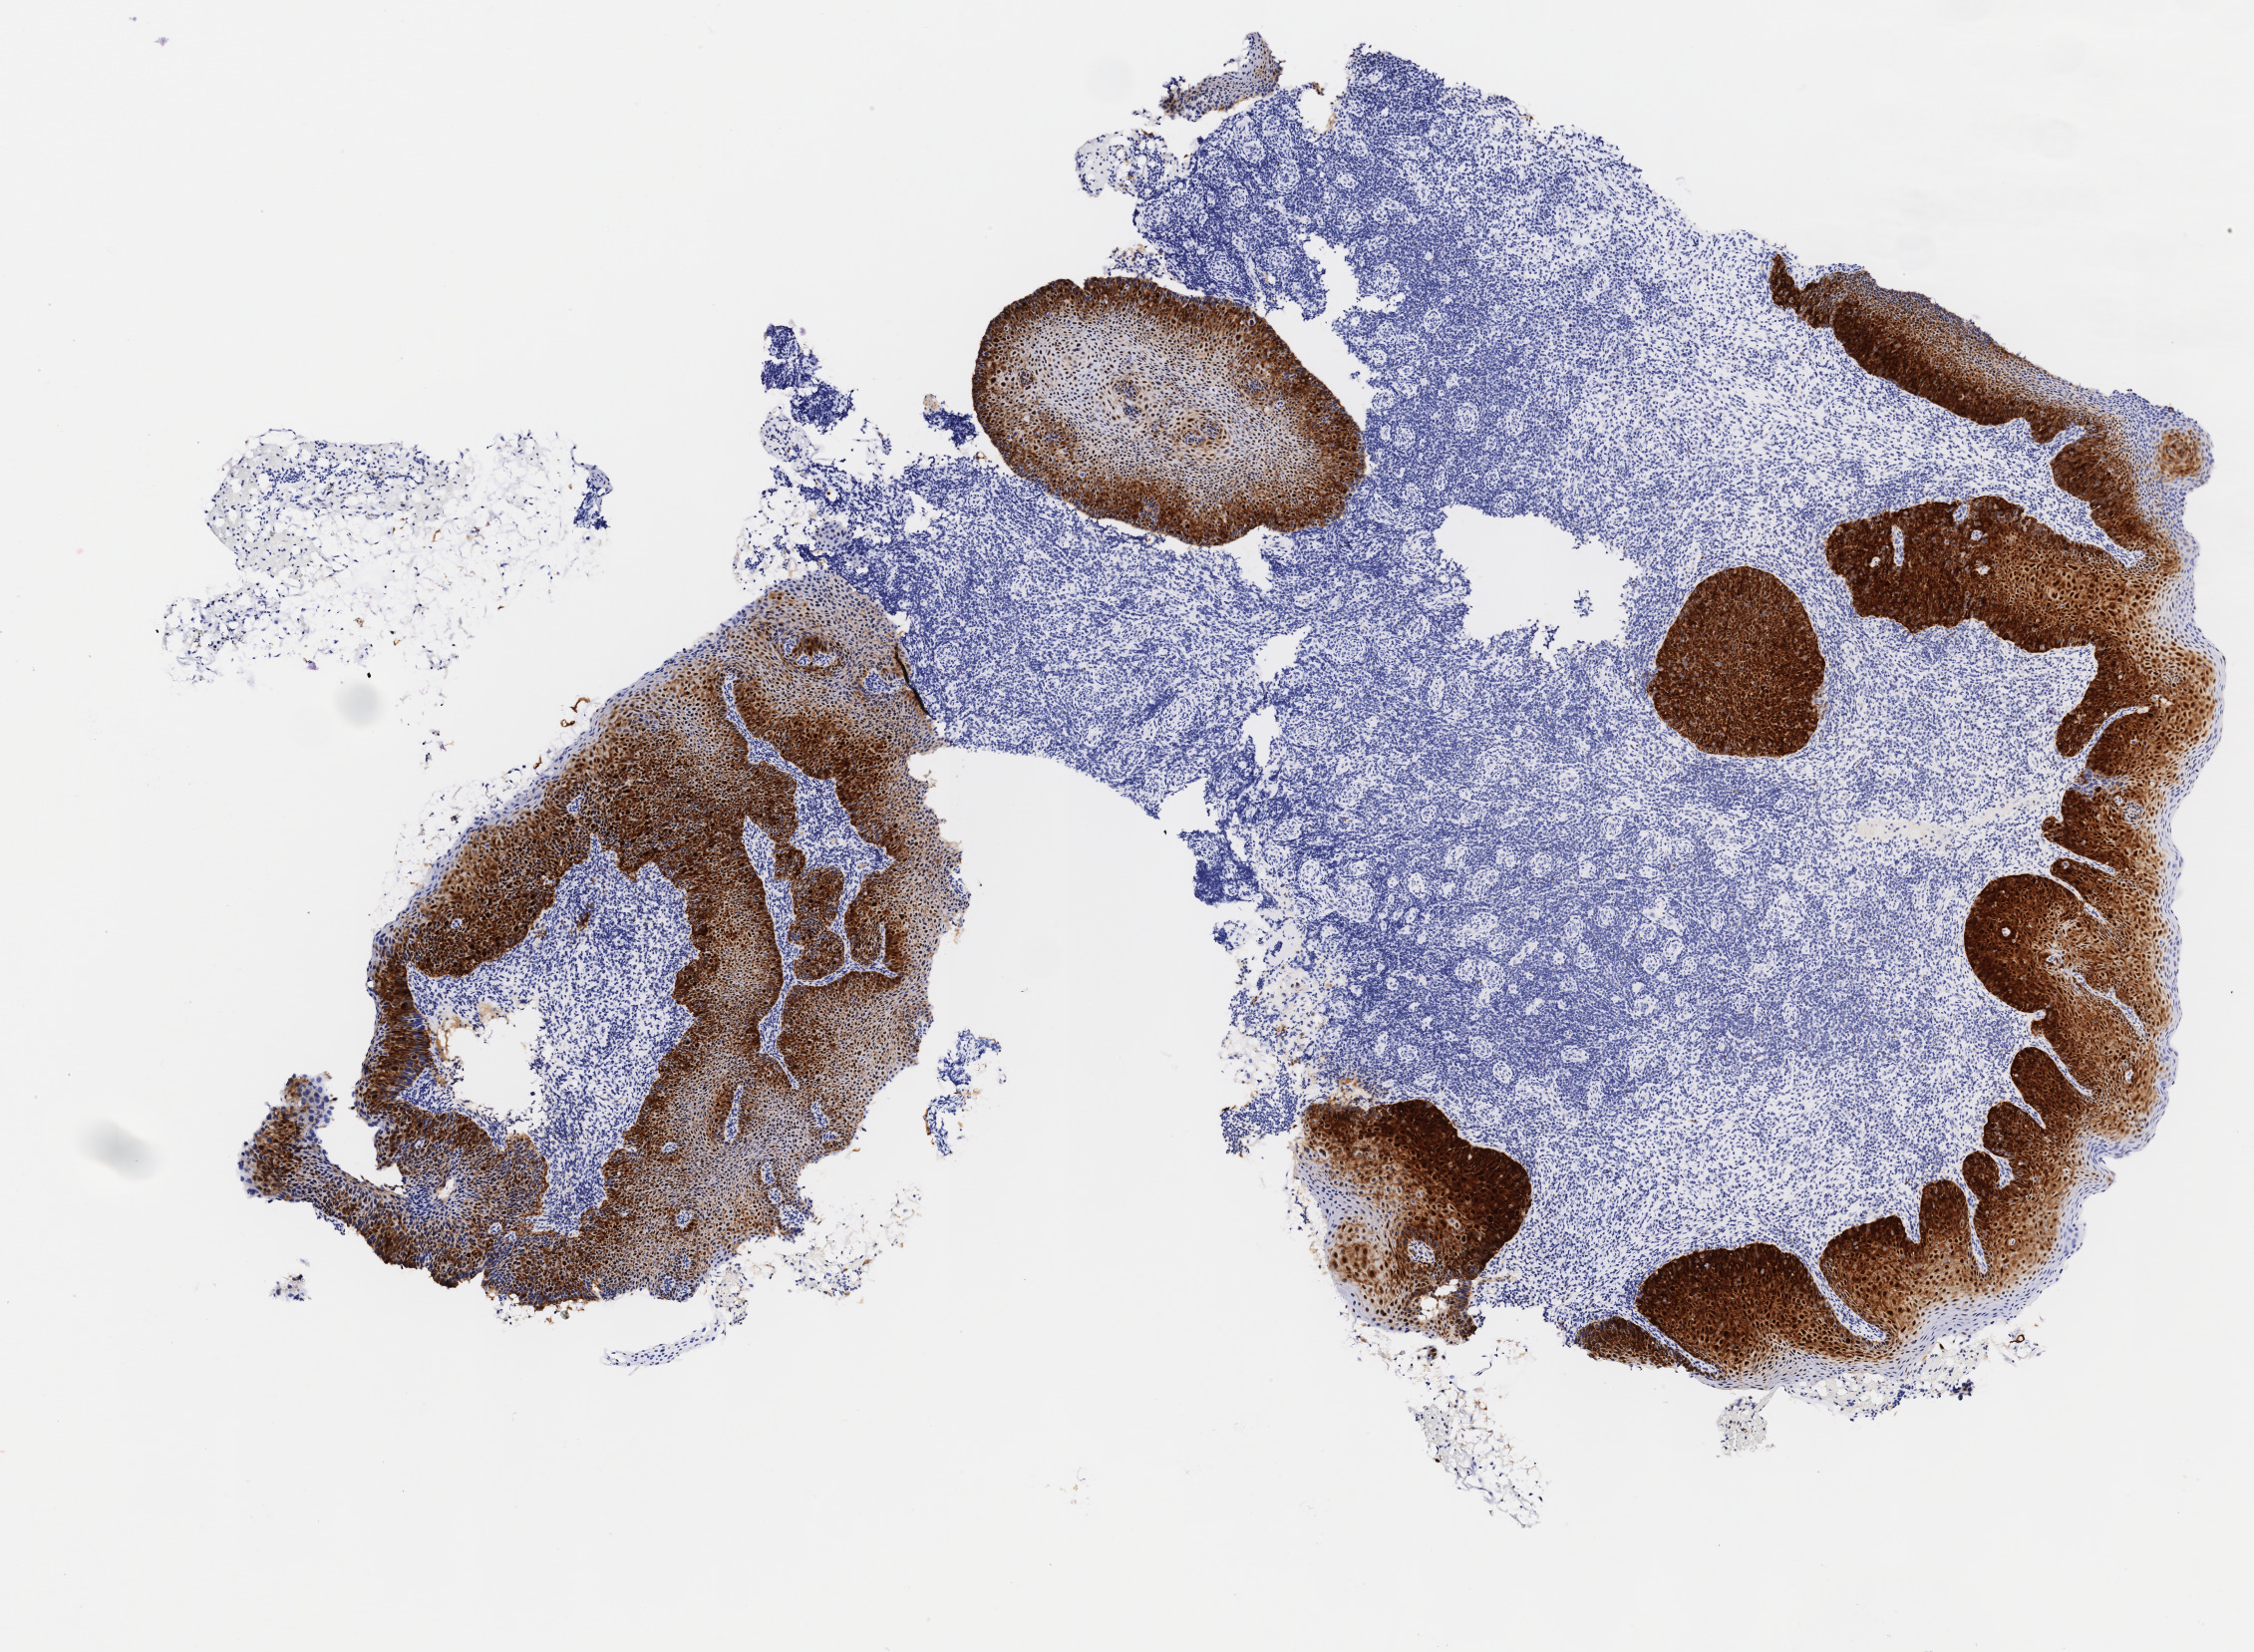
Whole-slide image, immunohistochemical stain for p16 (p16INK4a) — whole scanned area (about 4.5 x 3.3 mm) shown as a low-resolution overview. Female patient, aged 43.
Specimen: tumor tissue; site: cervix.